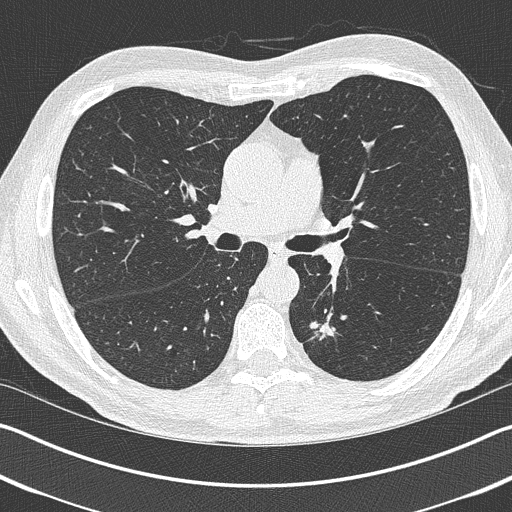
Low-dose screening chest CT, one axial slice; position 246 of 402 along the scan axis; lung window (W 1500 / L -600 HU); 512 × 512 image matrix.
Annotated regions visible in this slice (manually delineated by an expert):
- lesion 1 (tumor, lower lobe of left lung): box from (x=310, y=322) to (x=335, y=340) px